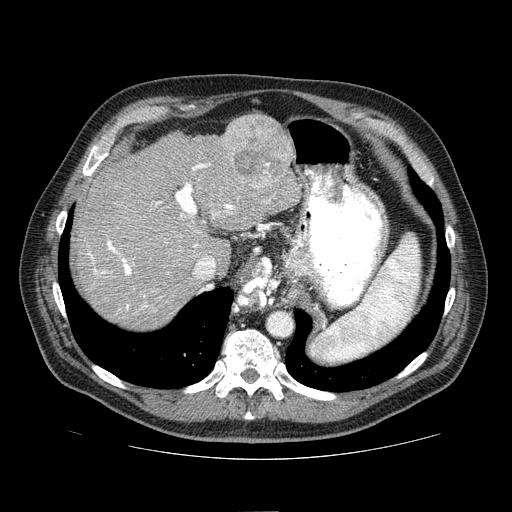
Contrast-enhanced abdominal CT (liver protocol), one axial slice. 100 kVp. One of 2 acquisitions stored at this slice position. Soft-tissue window (W 400 / L 40 HU). 512 × 512 image matrix, field of view 400 × 400 mm. From the clinical record (not read from this slice): diagnosis: hepatocellular carcinoma (patient treated with transarterial chemoembolisation; whether this scan precedes or follows treatment is not stated here); TNM stage (as recorded): Stage-IIIA.
Structures marked on this image (semi-automatic segmentation, software-assisted and operator-edited):
- abdominal aorta: bounding box <270,314,293,336> (left, top, right, bottom; pixels)
- liver parenchyma outside the tumour (the mass and vessels are separate outlines, so this box may not span the whole liver): <74,114,300,328>
- mass: <218,115,293,189>
- liver vessels: <88,163,271,310>